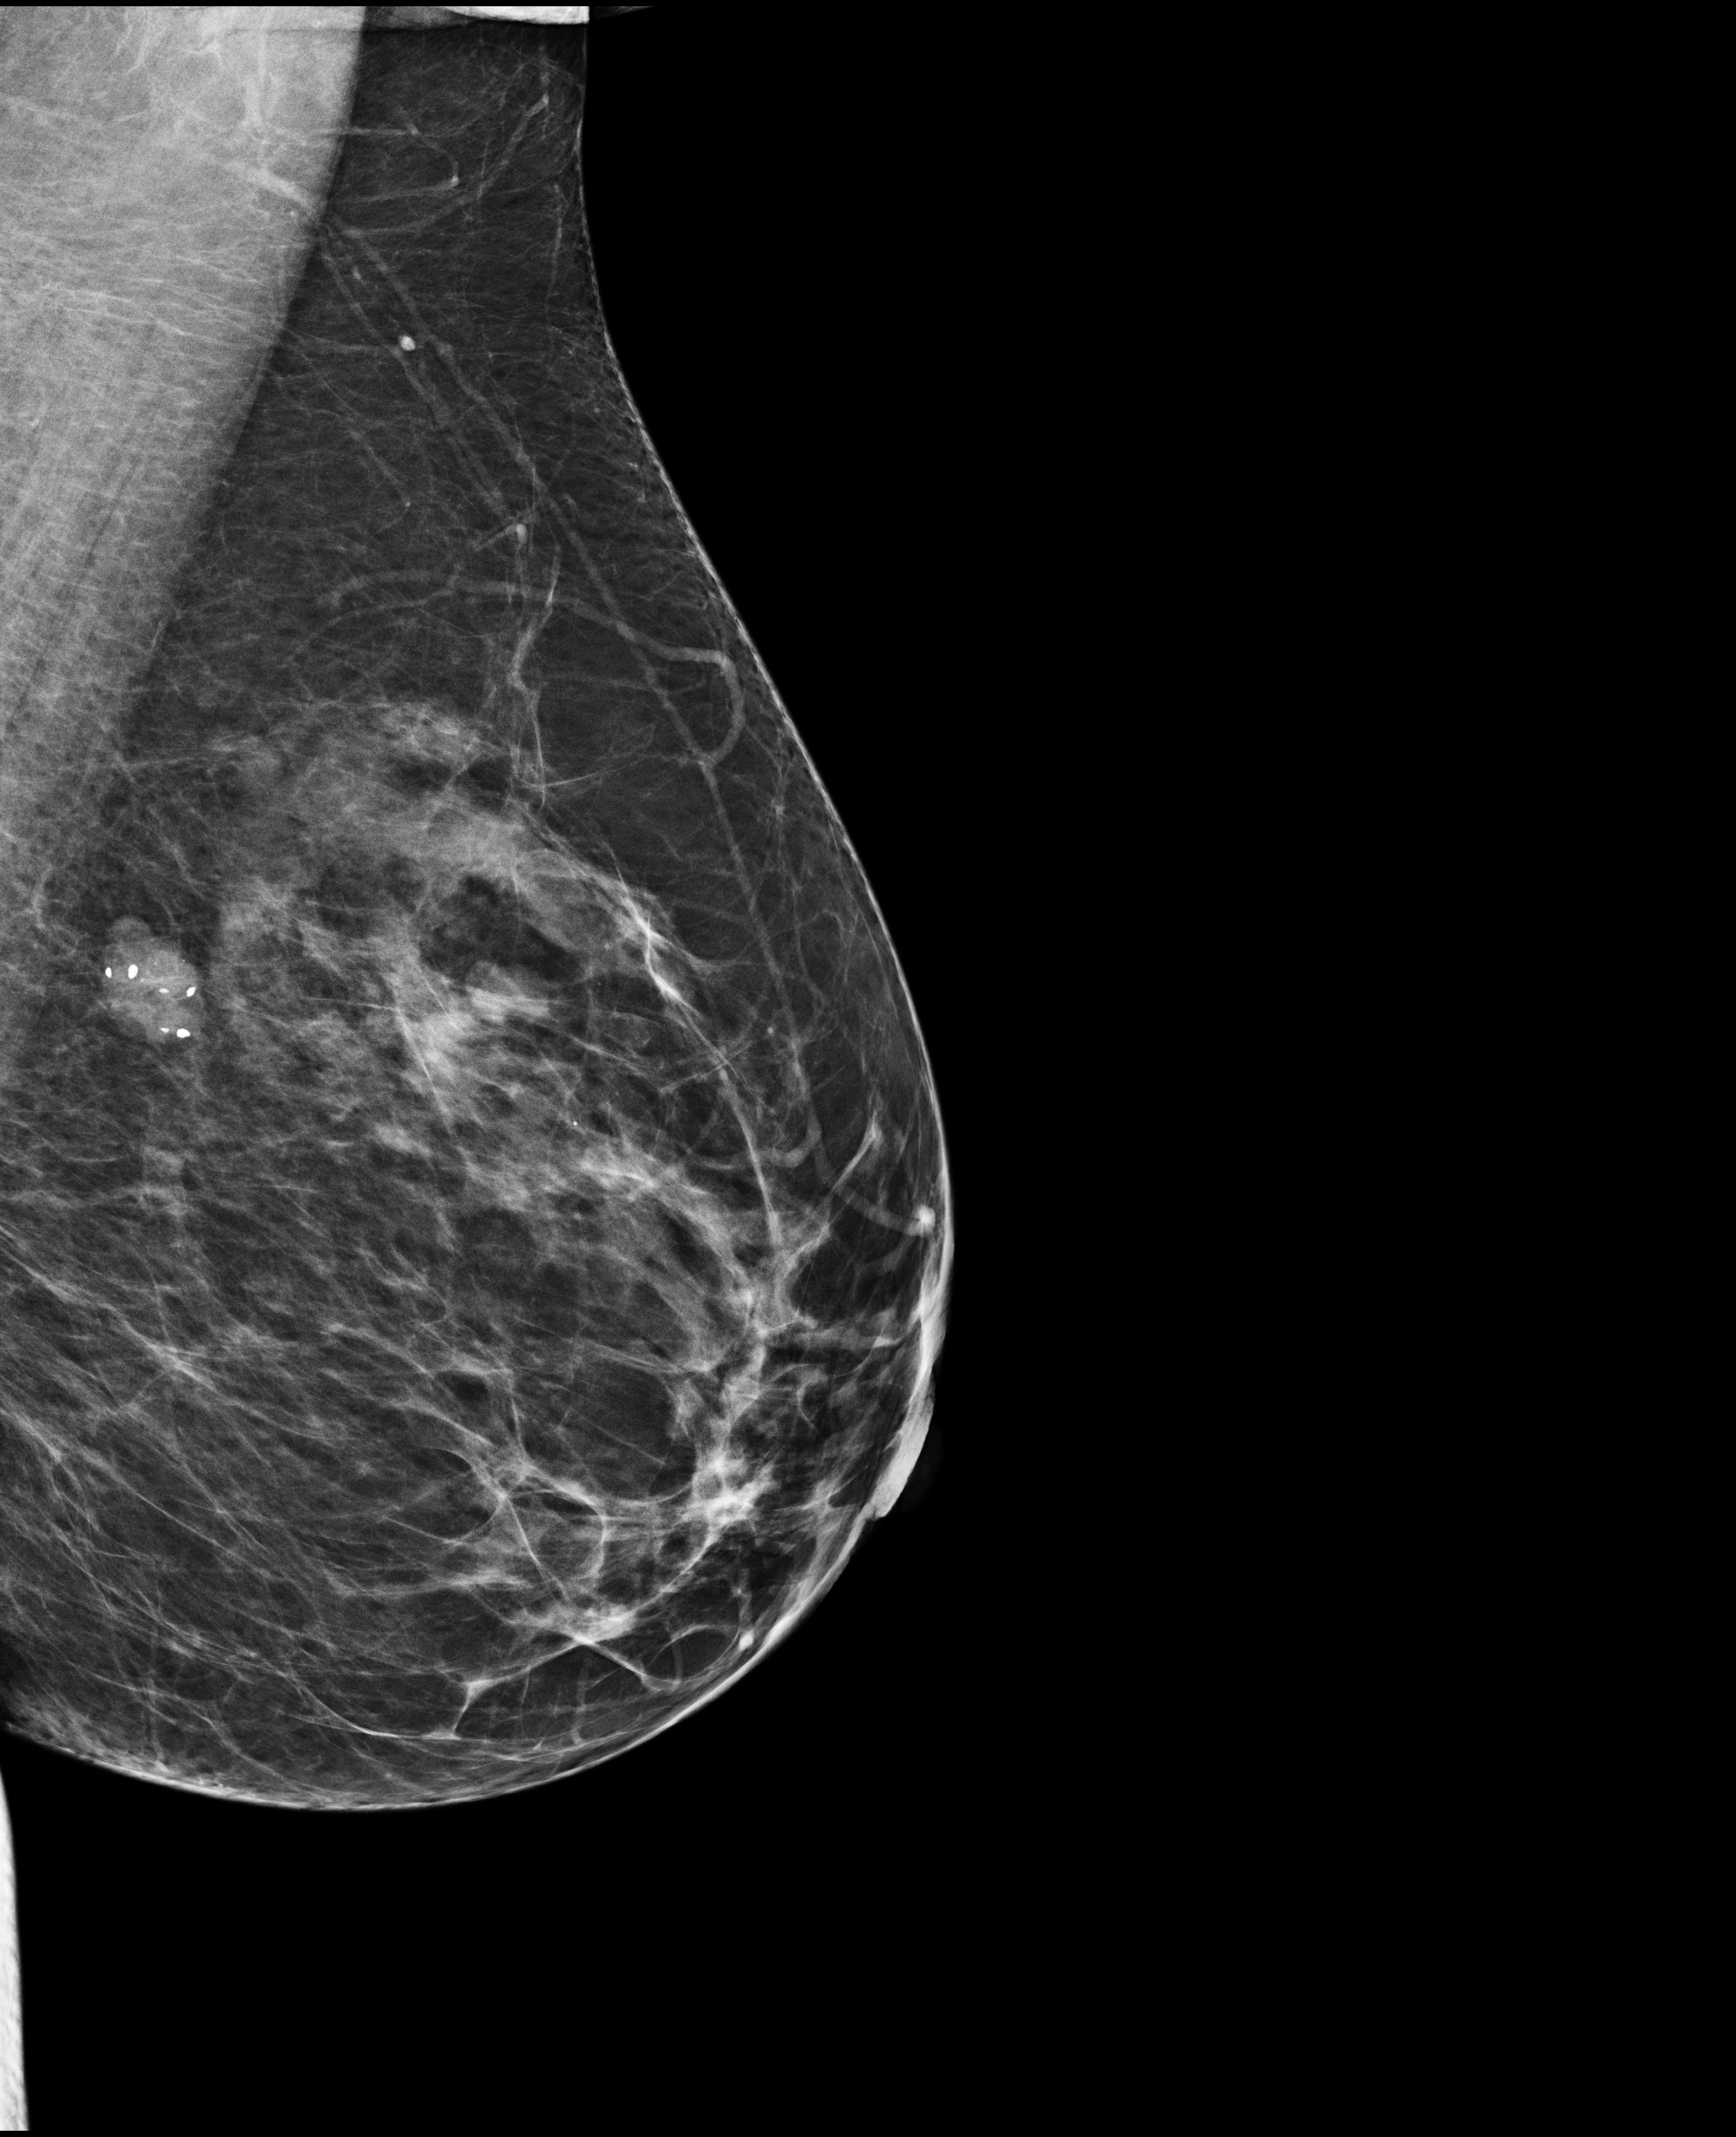
Screening examination, compressed breast thickness 61 mm. Female patient, age 65 years.
Image type: full-field digital mammogram. Breast: left. Projection: medio-lateral oblique projection.